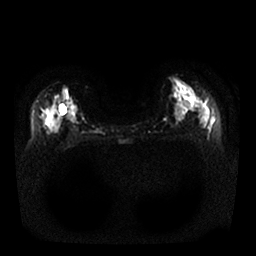
Breast MRI, one axial slice; slice 13 of 25 in the series (ordered by position); diffusion-weighted series; image 2 of 4 stored at this slice position (different b-values; order by instance number); 1.5 T; 4 mm slice thickness; 256 × 256 image matrix, field of view 340 × 340 mm. Female patient.
Outlined on this slice (outlined manually by an expert reader):
- tumour on diffusion-weighted imaging: bounding box <47,120,56,128> (left, top, right, bottom; pixels)